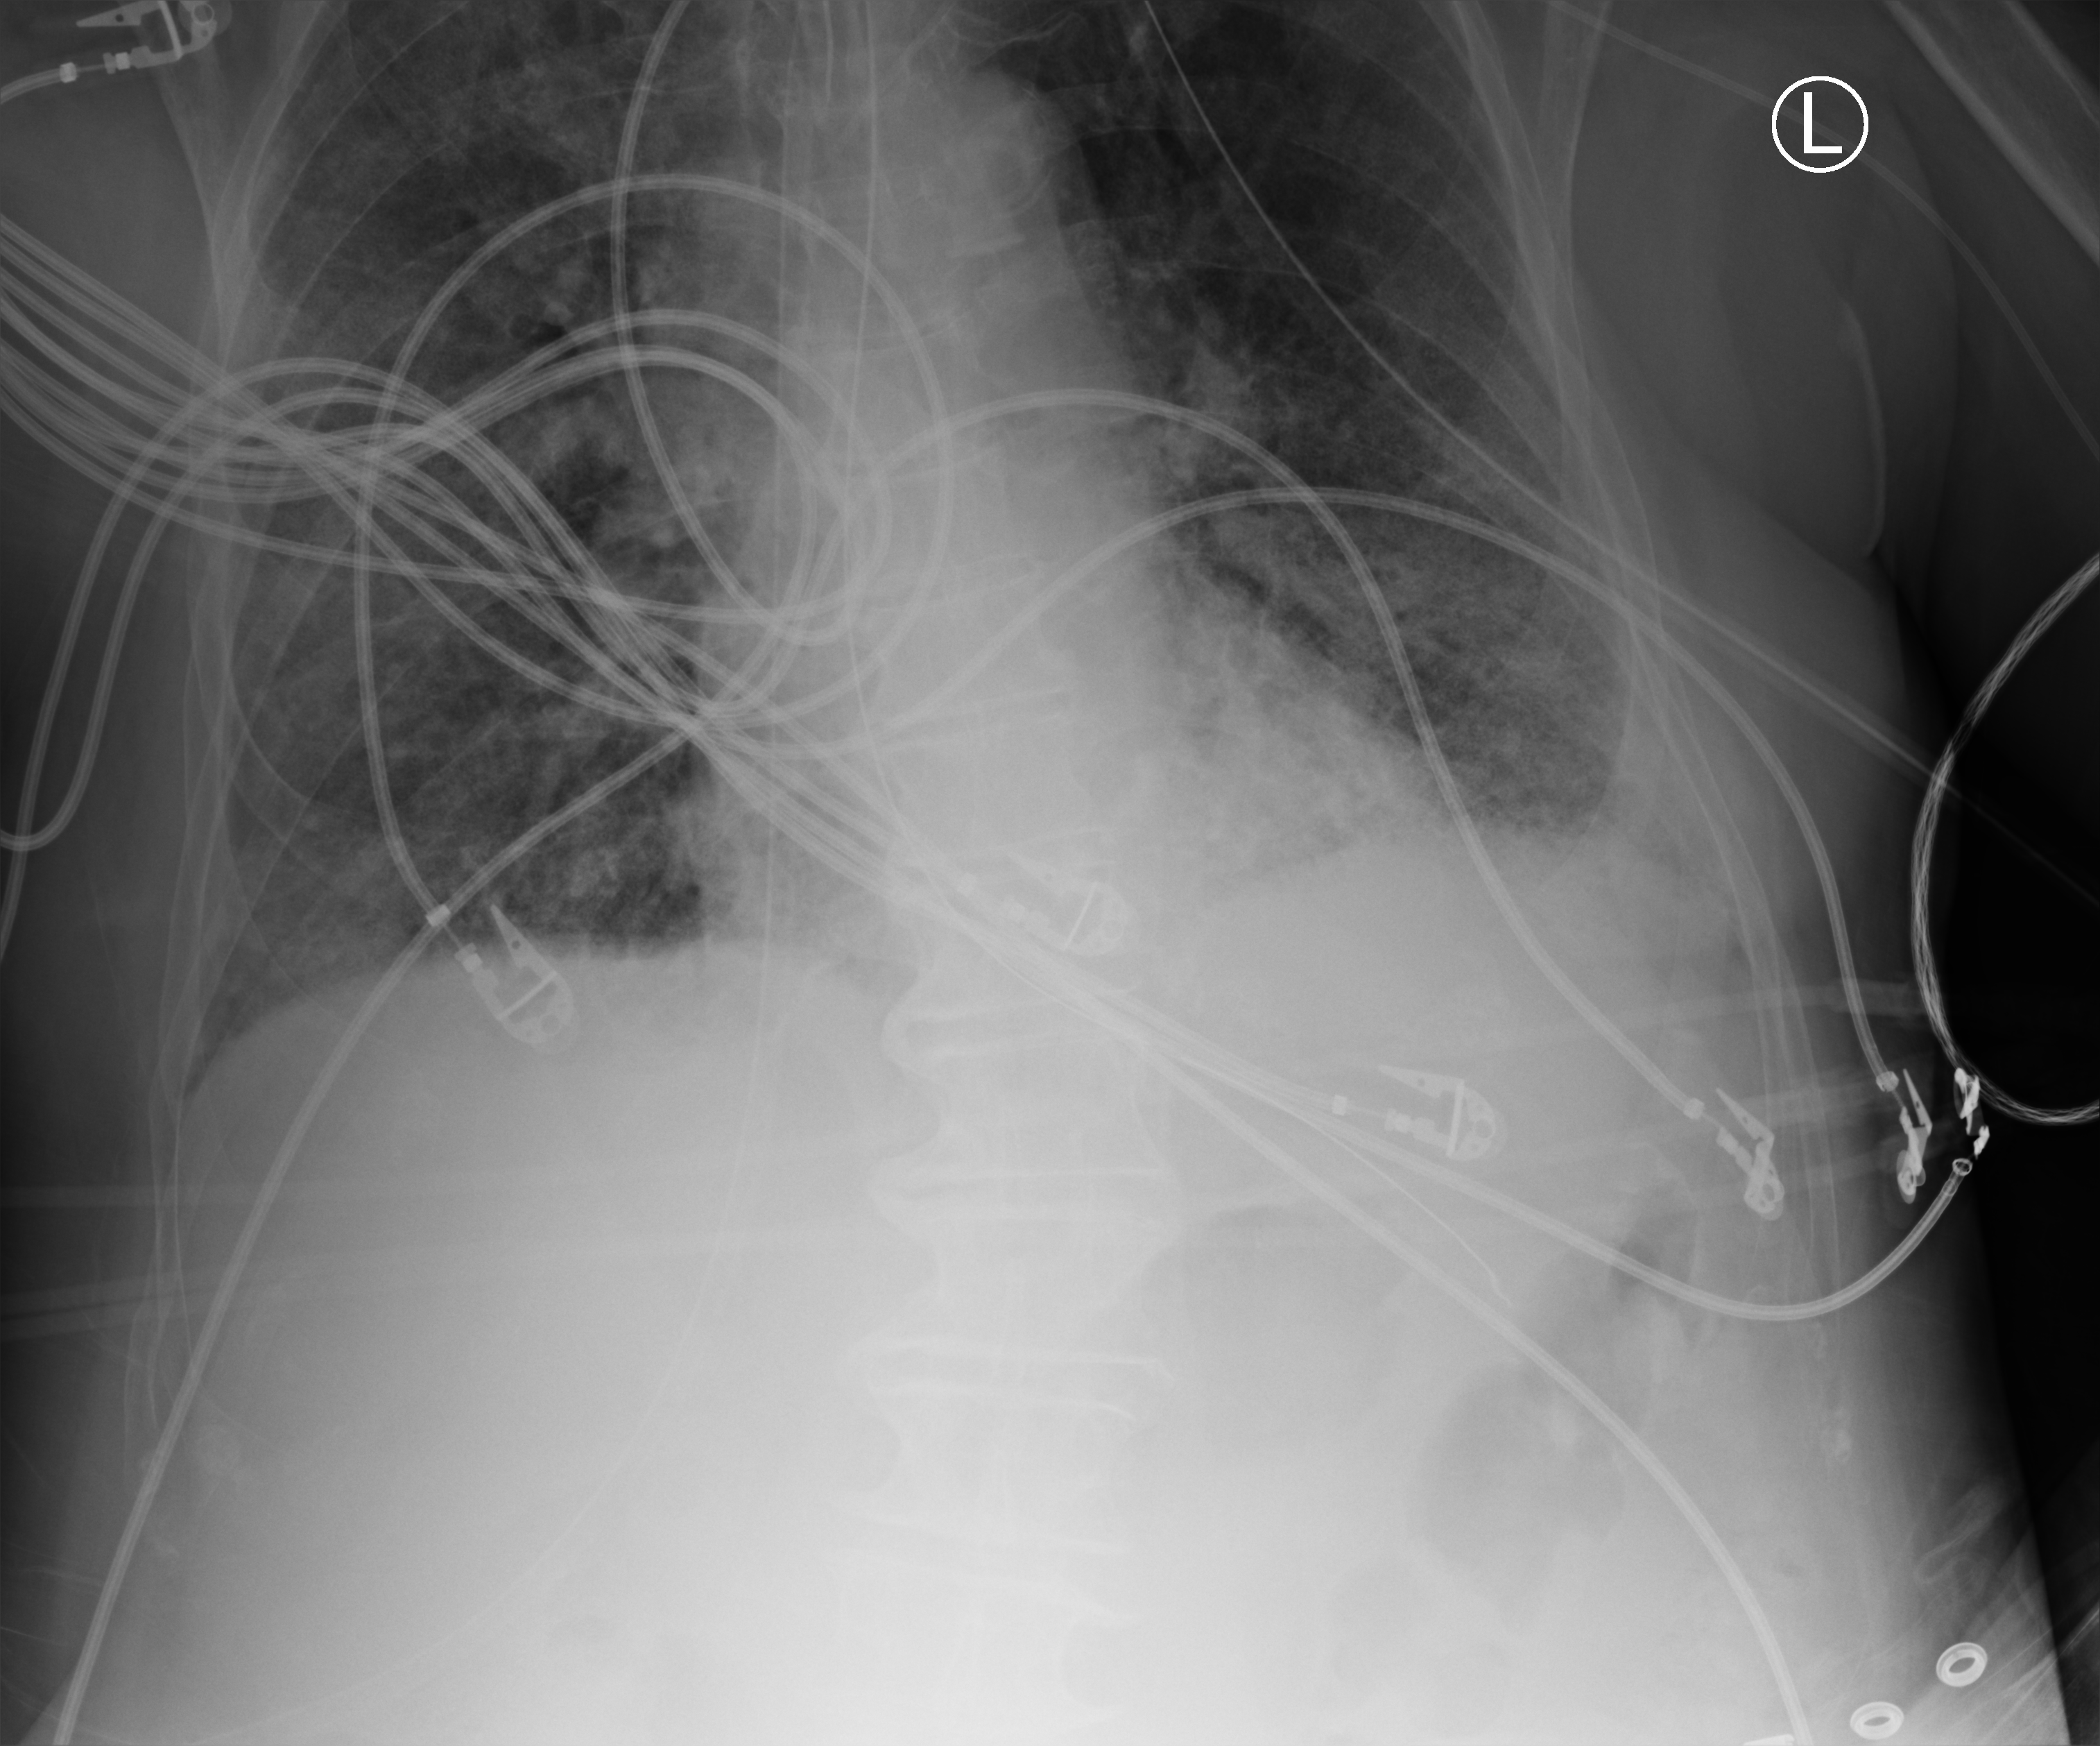
Portable chest radiograph; anteroposterior (AP) projection. Male patient hospitalised with COVID-19, age 75–90 years.
Hospital-stay facts (about this admission, not read from this image; timing relative to this image not recorded): mechanically ventilated during this hospital stay: yes; admitted to intensive care during this hospital stay: yes.